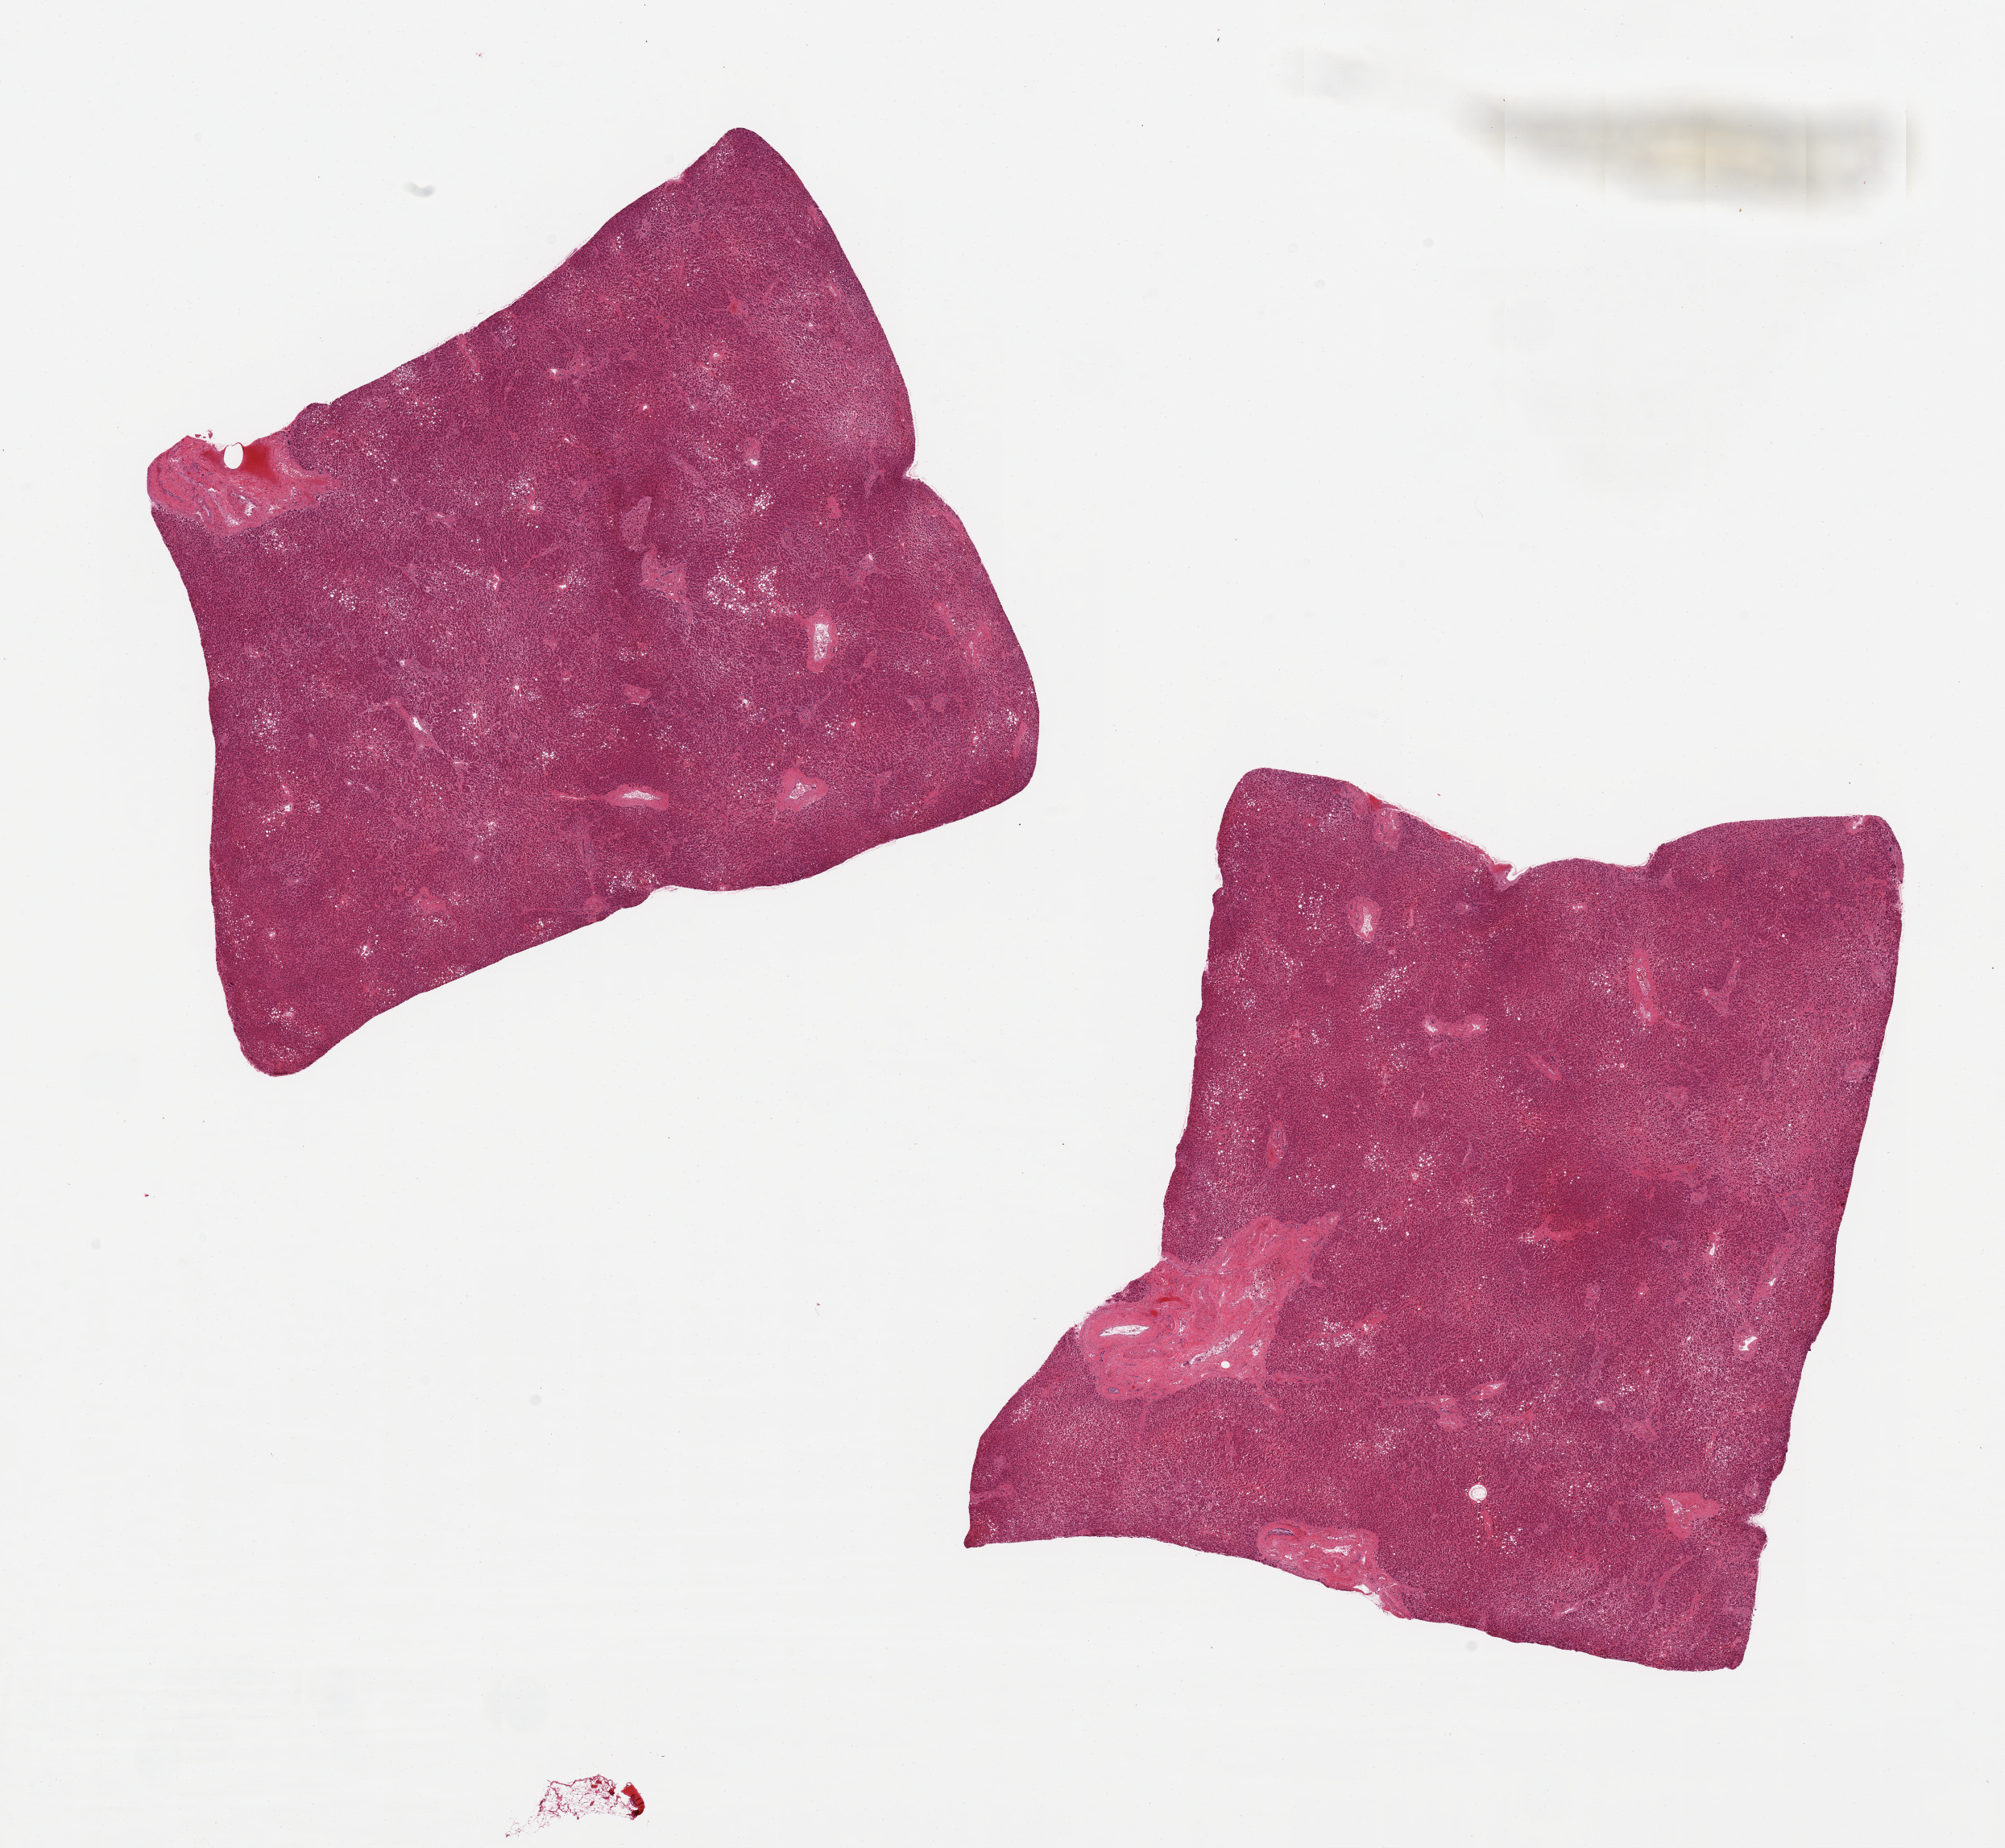
Digitized H&E-stained section, brightfield — low-resolution overview of the scanned area, about 19.7 x 18.1 mm (slide scanned at 20x), PAXgene-fixed, paraffin-embedded tissue, section of liver (target tissue), donor tissue sample.
Review note (as recorded): 2 pieces; 10% macrovesicular steatosis.